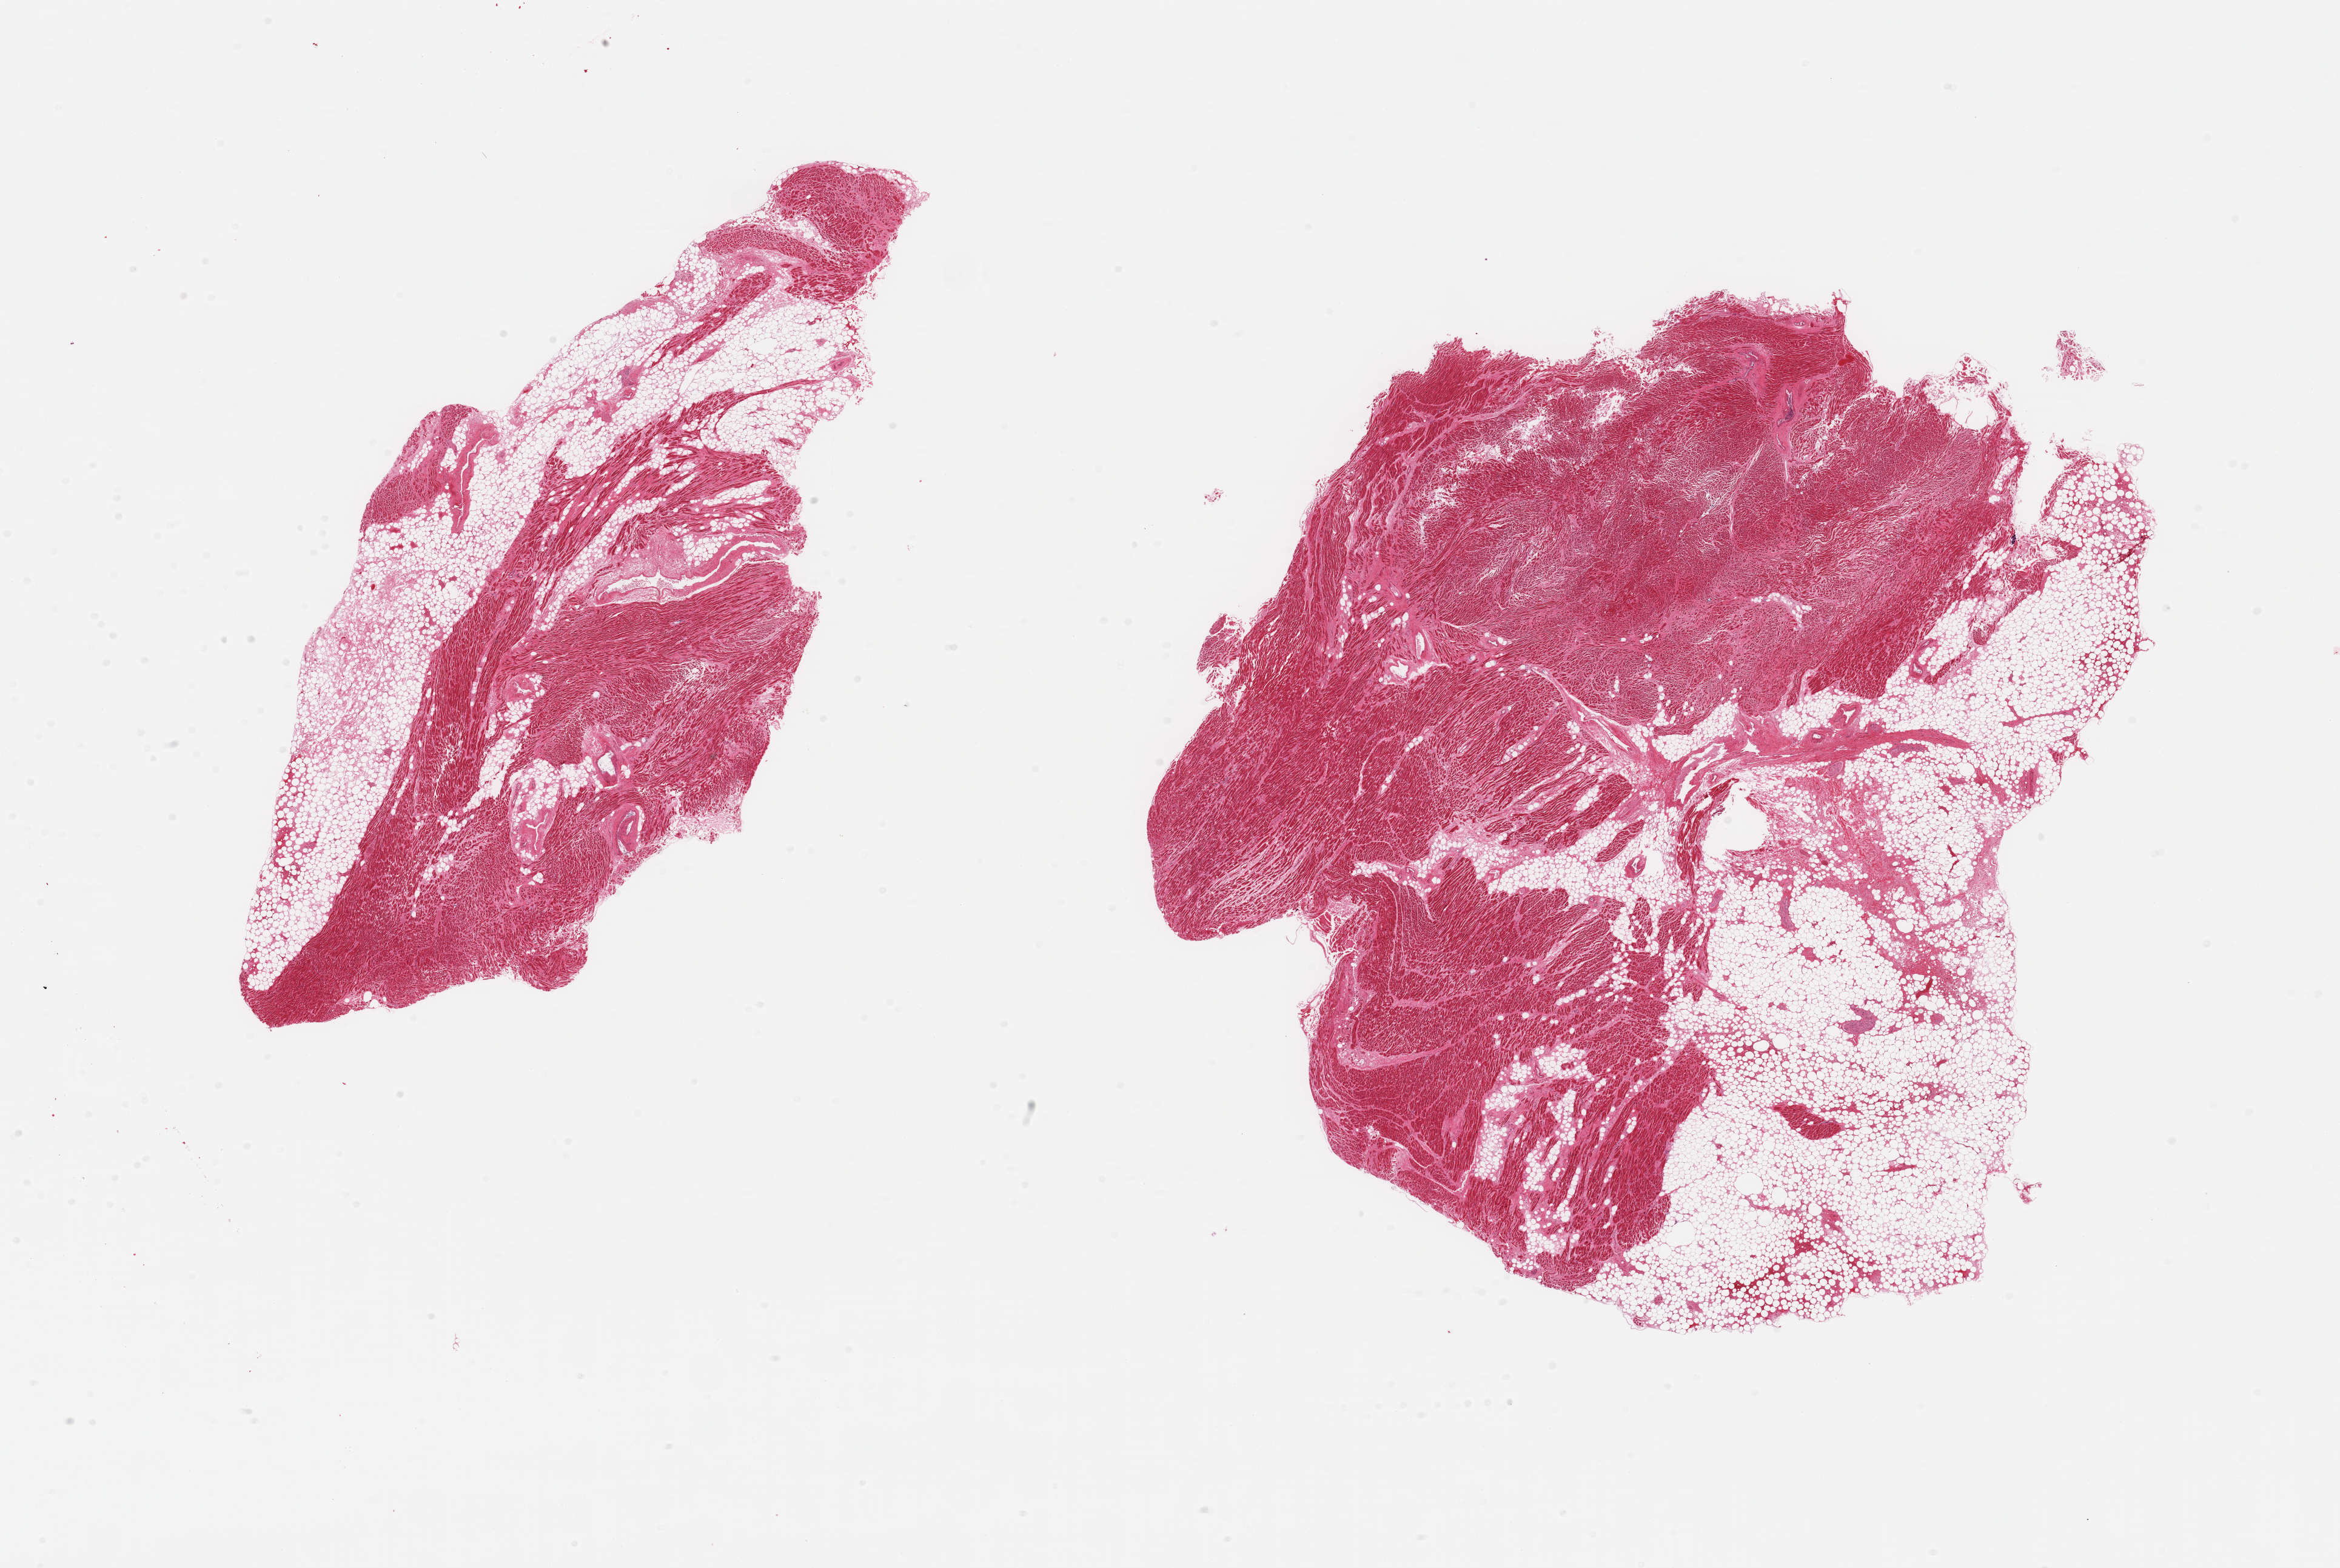
Digitized H&E-stained section, brightfield — low-resolution overview of the scanned area, about 30.5 x 20.5 mm (acquisition: 20x scan); PAXgene-fixed paraffin-embedded (PFPE) section; sampled site (target tissue): auricular appendage; tissue donor sample. Donor sex: male.
Review note (as recorded): 2 pieces, focal fat necrosis.